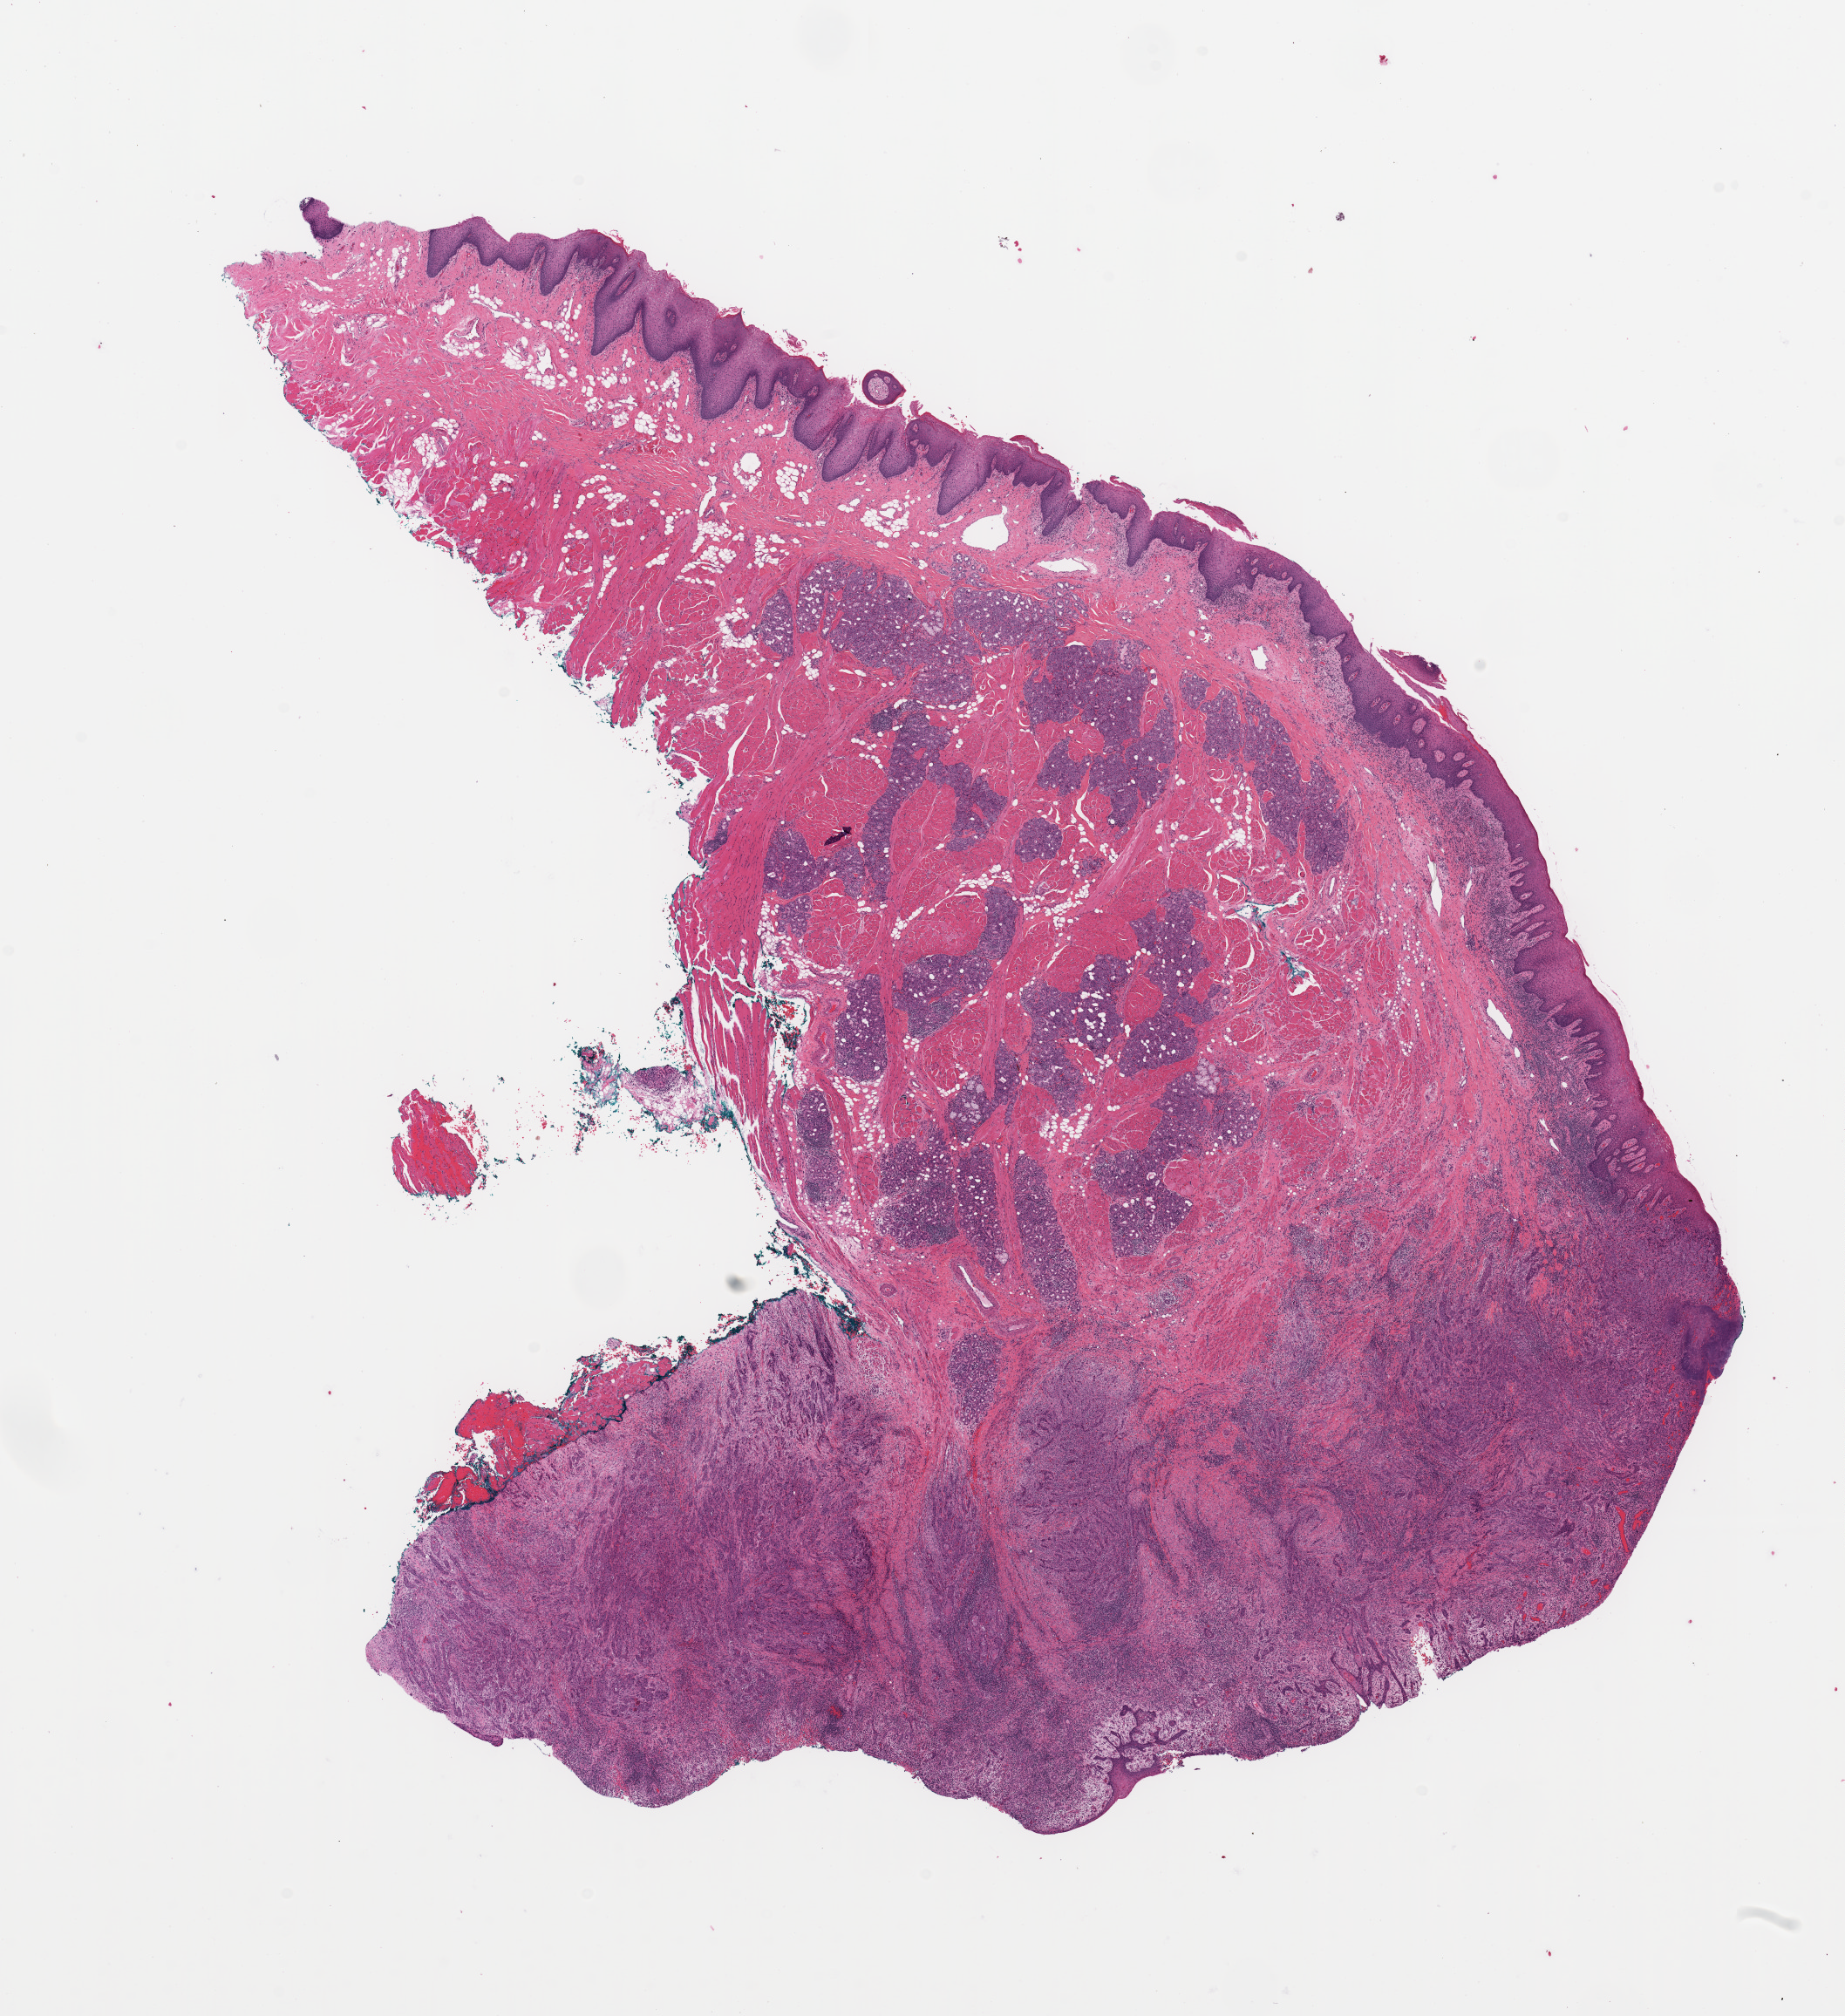
Whole-slide histology image, Hematoxylin and eosin (H&E) stained, a low-resolution overview of the entire scanned area, about 16.7 x 18.3 mm (acquisition: 20x scan), head and neck, tissue type not recorded. 50-year-old male patient.
Patient diagnosis: Squamous cell carcinoma, NOS (tongue, NOS).